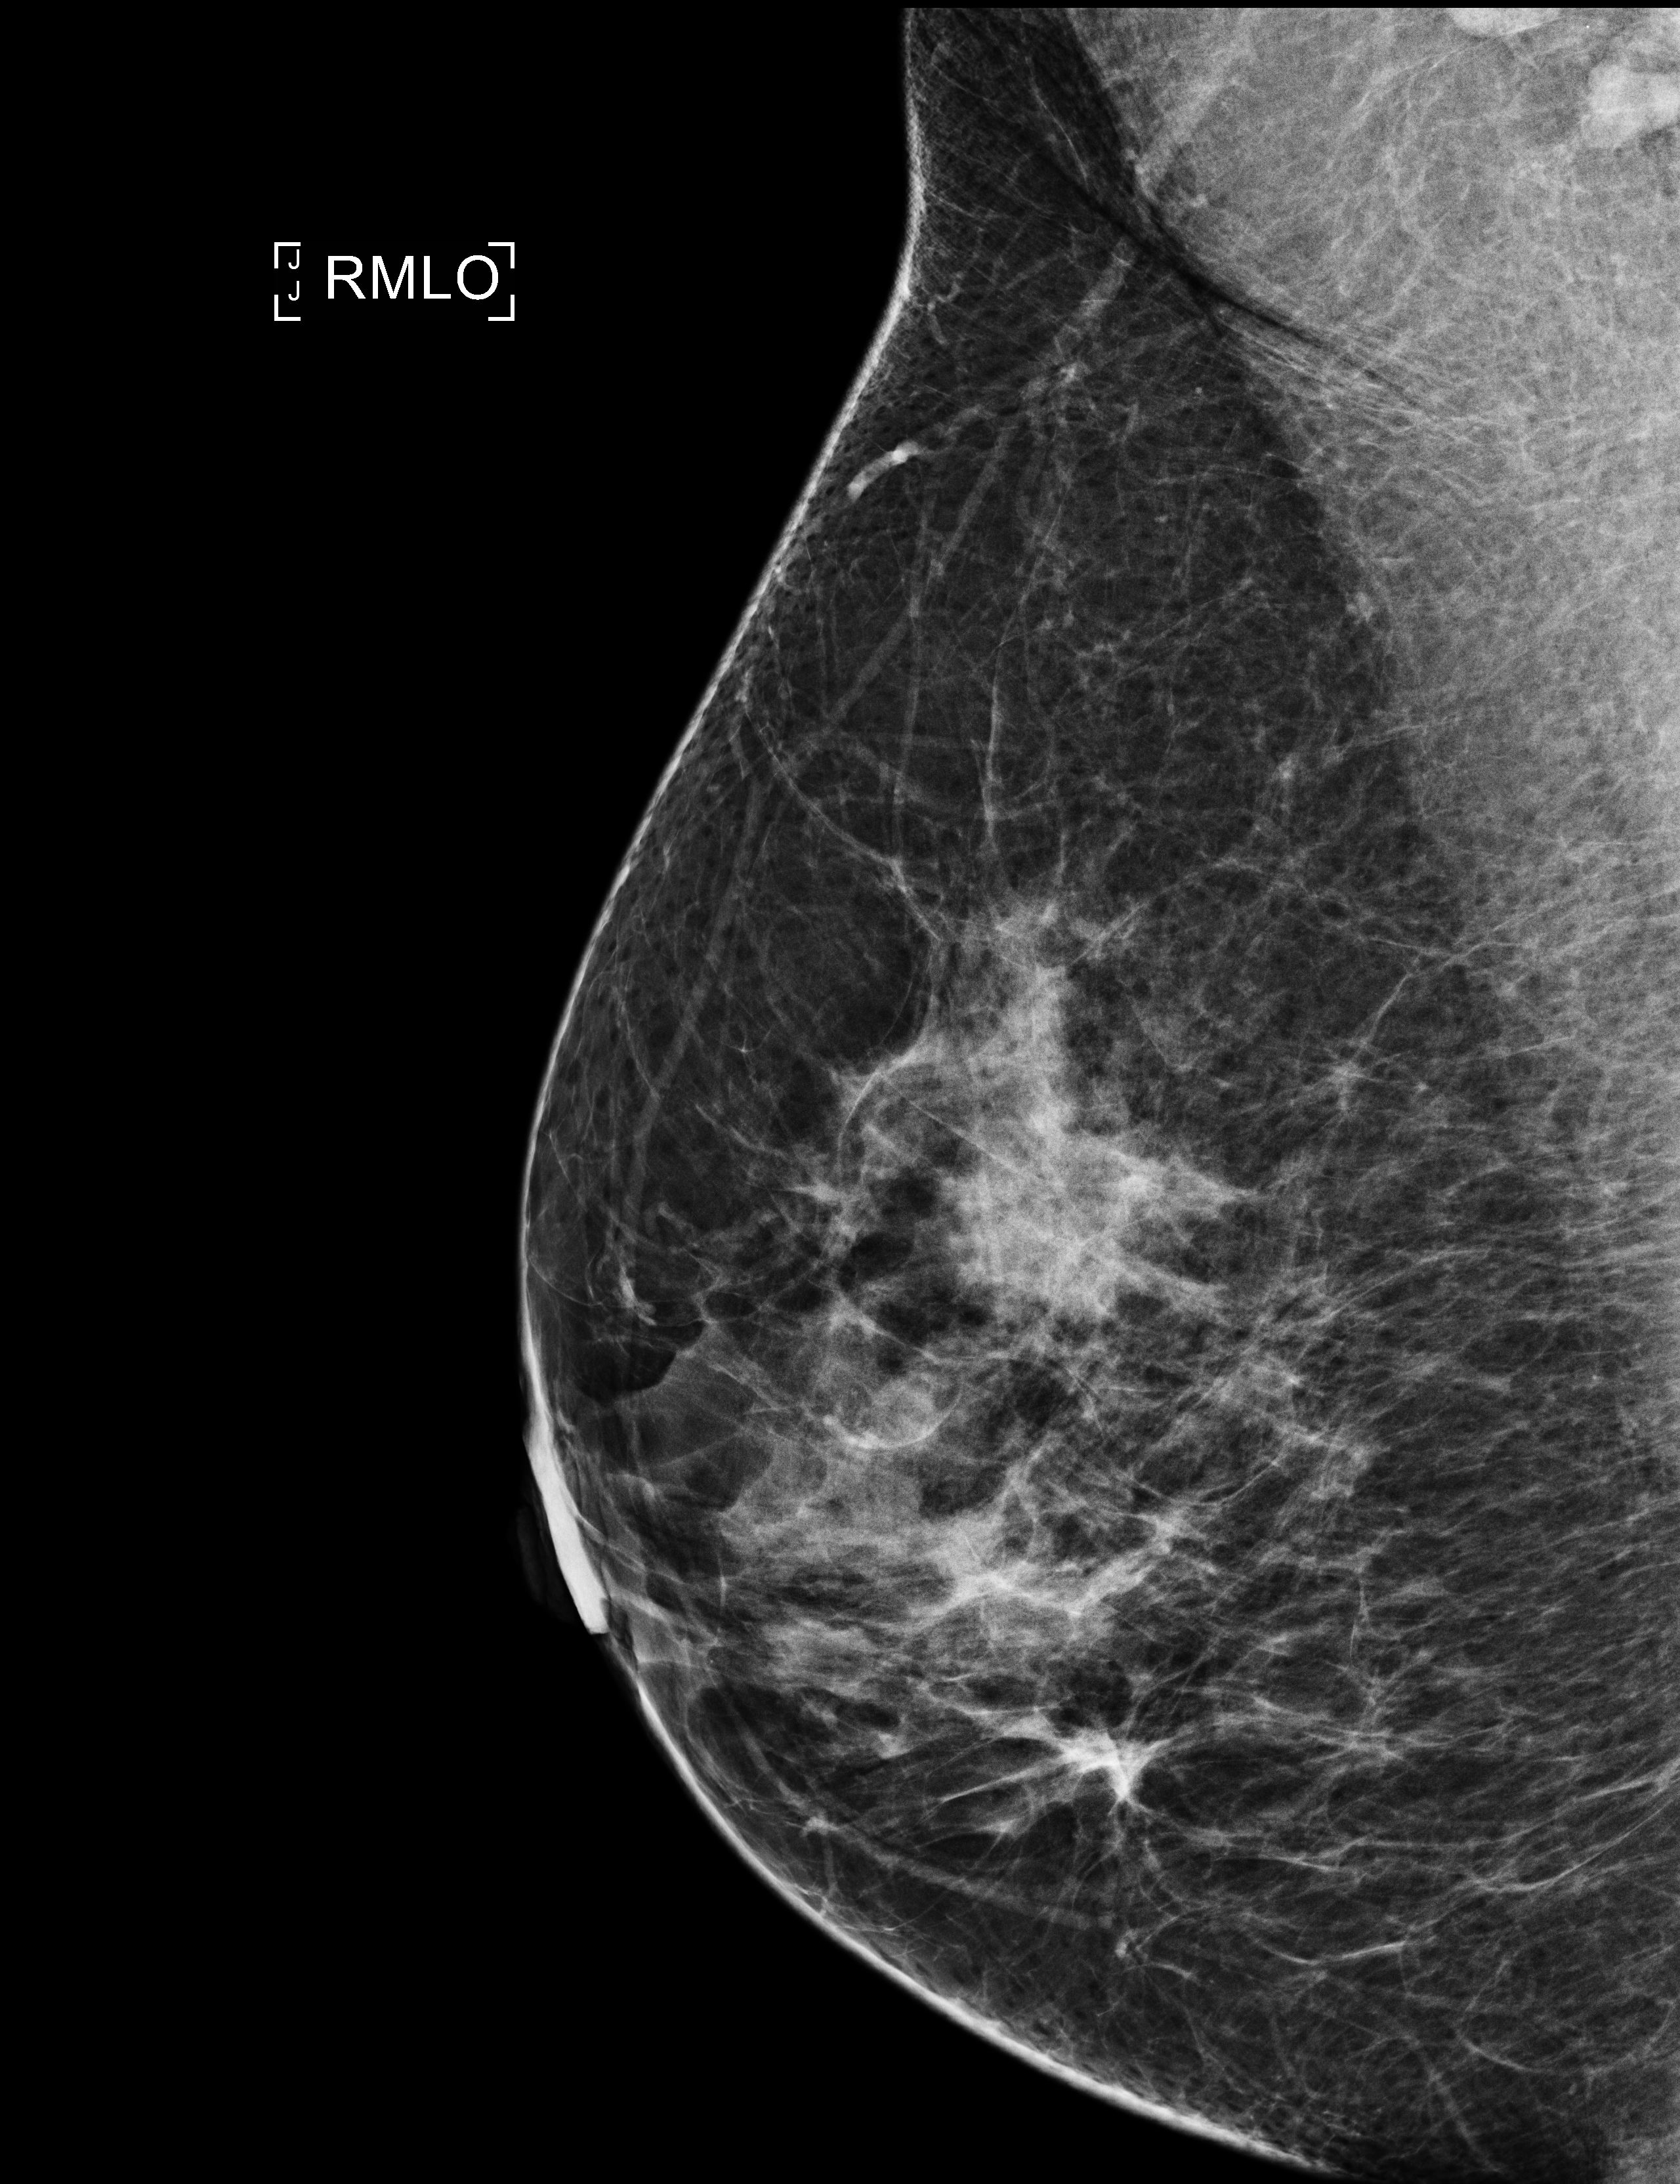
Screening examination; compressed breast thickness 67 mm. Patient: female, 53 years.
Image type: full-field digital mammogram. Breast: right. Projection: medio-lateral oblique projection. BI-RADS breast density category at the screening exam (both breasts, scale 1–4): 2. Final BI-RADS assessment for this screening round (tomosynthesis exam, both breasts): category 1. Recall: no recall after this screen.